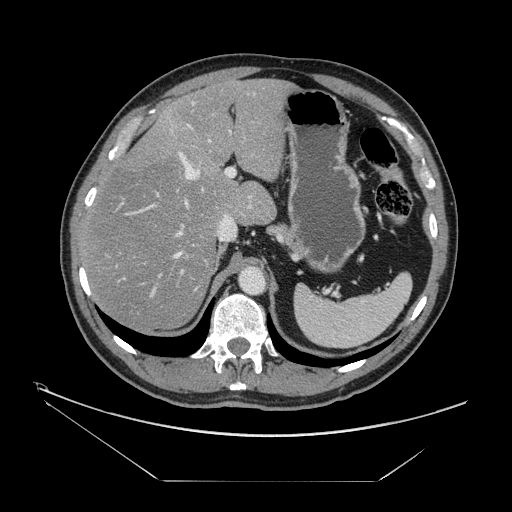
Contrast-enhanced abdominal CT, one axial slice. Position 101 of 161 along the scan axis. 120 kVp. Intravenous contrast given. Soft-tissue window (W 400 / L 40 HU). 2.5 mm slice thickness. 512 × 512 image matrix, field of view 440 × 440 mm. Male patient, age 65 years. Case-level facts recorded for this patient, not image findings: diagnosis: colorectal cancer liver metastases, imaged before liver resection; multiple liver metastases: yes; largest metastasis: 4.2 cm; disease in both lobes: yes.
Structures marked on this image (outlined manually by an expert reader):
- hepatic veins: bounding box (x1, y1, x2, y2) in pixels: (122, 125, 210, 280)
- liver: (82, 80, 290, 329)
- planned liver remnant (the part of the liver to remain after resection): (81, 80, 290, 329)
- portal vein (with intrahepatic branches): (114, 93, 255, 299)